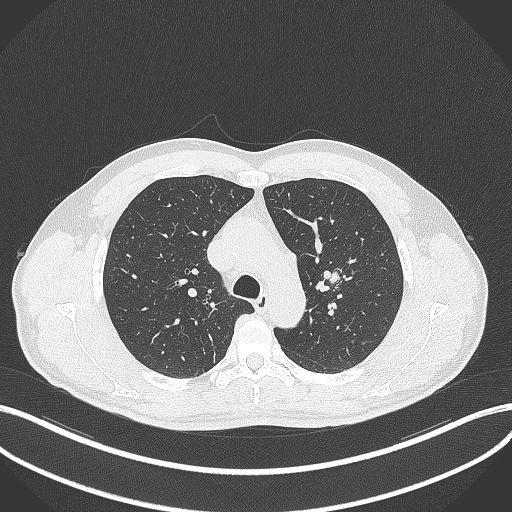
Chest CT, one axial slice. Slice 302 of 392 in the series (ordered by position). Reconstruction kernel B70f. 120 kVp. Lung window (W 1500 / L -600 HU). 1 mm slice thickness. 512 × 512 image matrix, field of view 400 × 400 mm. Male patient, age 50 years. Case-level facts recorded for this patient, not image findings: clinical TNM (as recorded): T1c N1 M1b.
Annotated regions visible in this slice (bounding box drawn by a radiologist):
- lung tumour (recorded histology: squamous cell carcinoma): bounding box <315,262,344,294> (left, top, right, bottom; pixels)